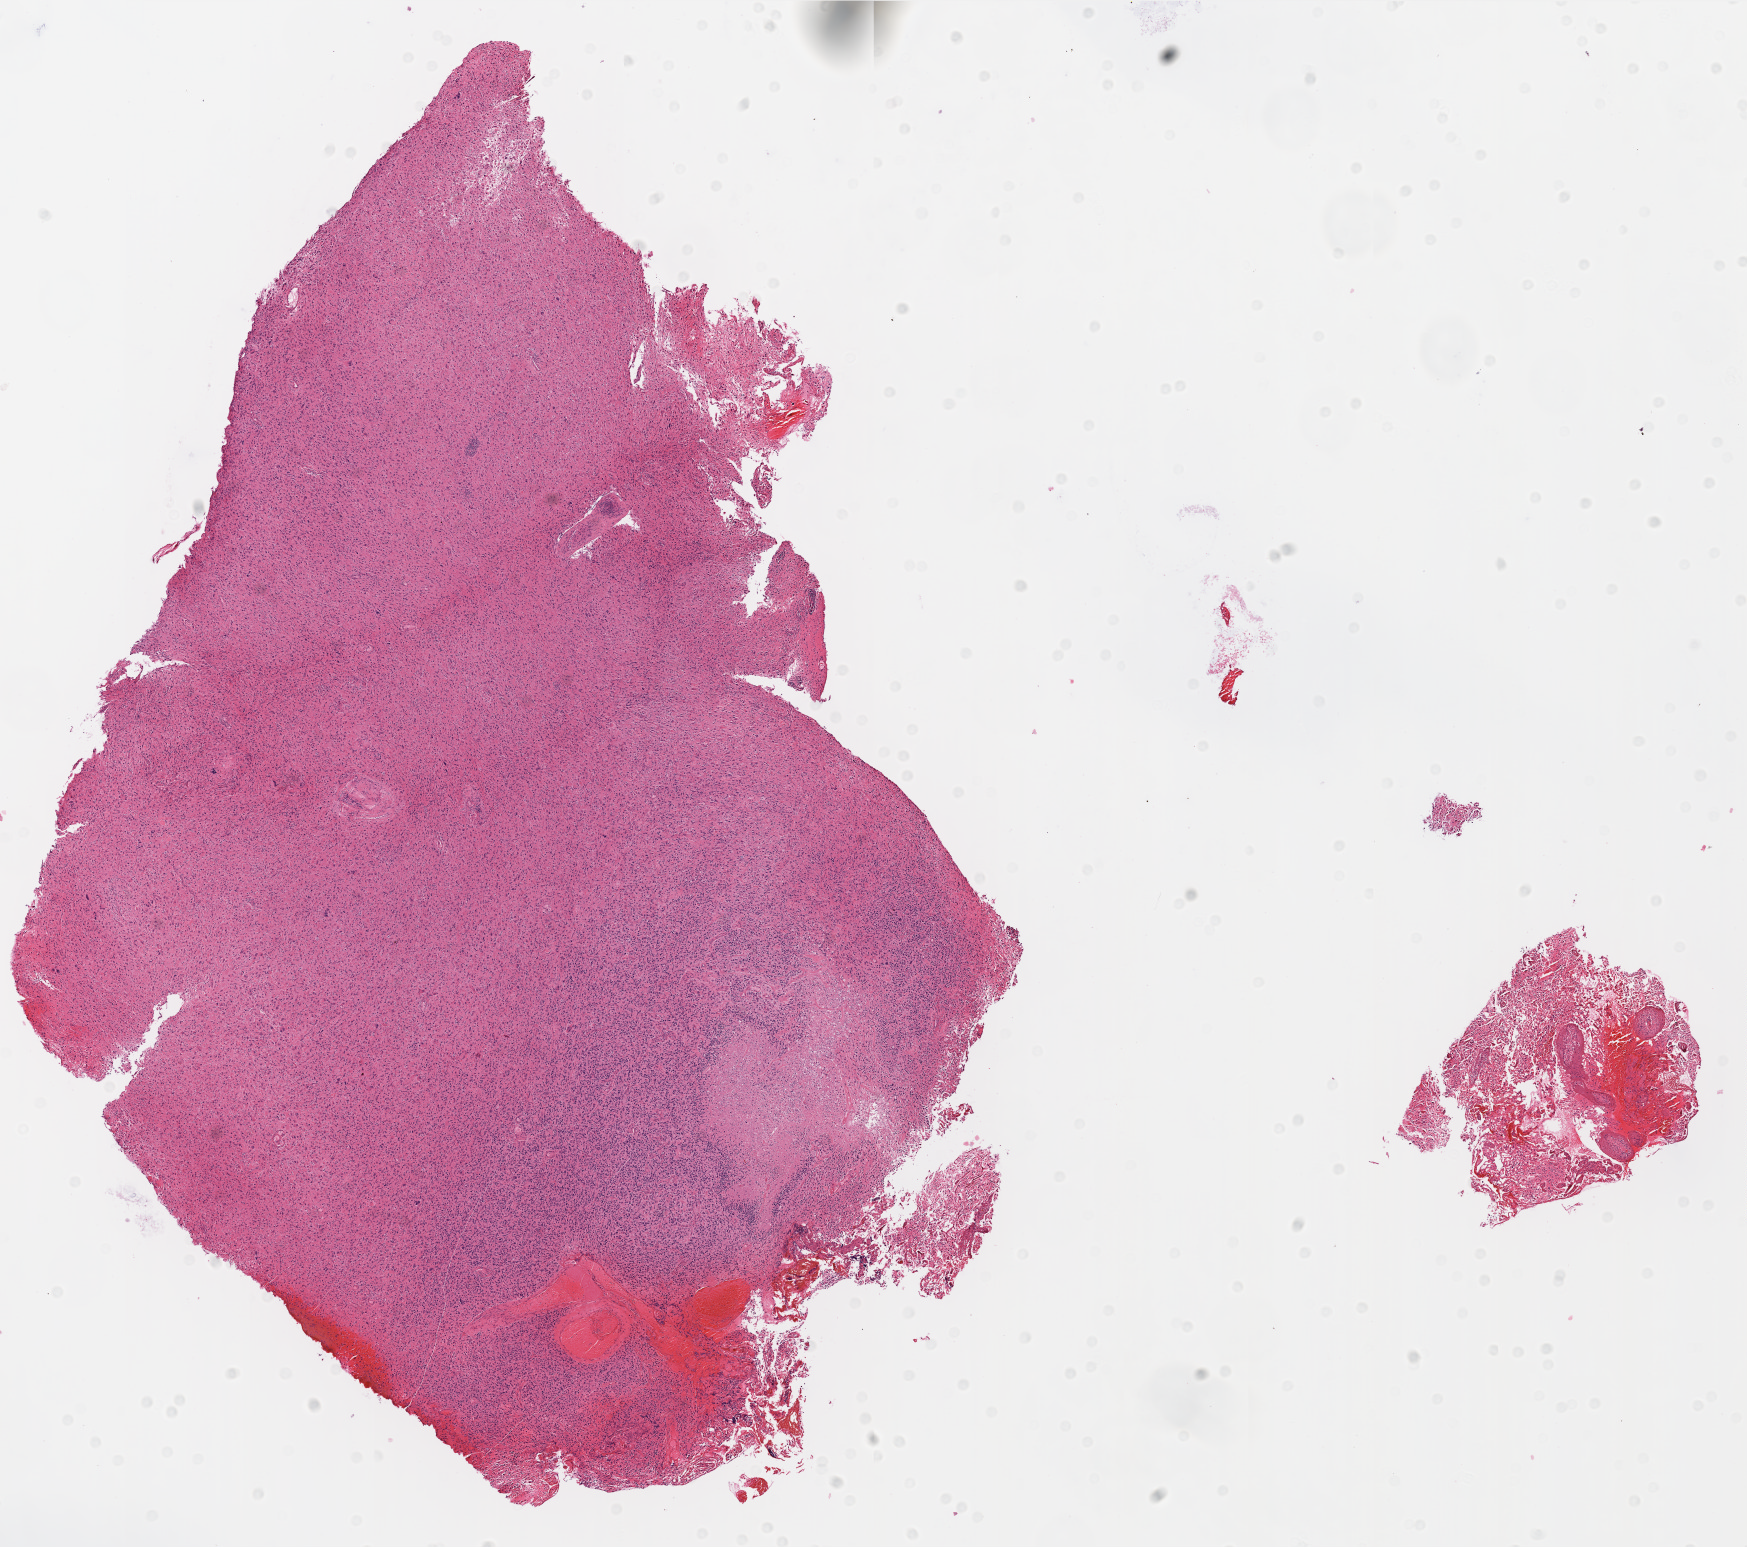
Whole-slide histology image, H&E-stained, a low-resolution overview of the entire scanned area, about 14.0 x 12.4 mm (from a 20x scan). Formalin-fixed paraffin-embedded (FFPE) diagnostic section. Sample: primary tumour, brain. Male patient; age at initial diagnosis 76 years.
* pathologic diagnosis: Glioblastoma